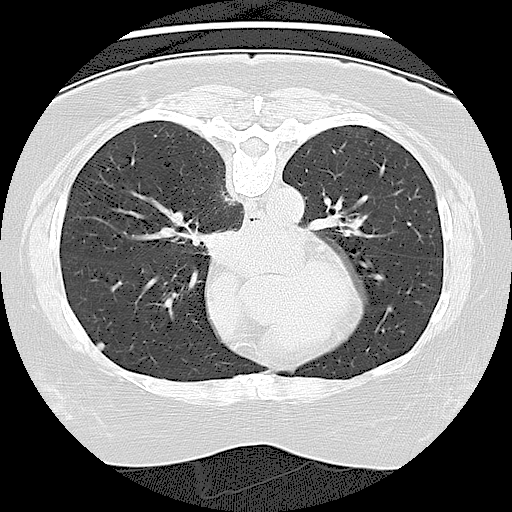
Axial slice from a low-dose chest CT screening exam, baseline screening round, lung window (W 1500 / L -600 HU), 120 kVp, slice 63 of 108 in the series. Female, age 67 years at enrolment. Former smoker at enrolment.
Expert-annotated lung lesion, bounding box [x1, y1, x2, y2] px = [80, 327, 123, 367]. The exam's reader record, not a measurement of the box and not confirmed to be the same lesion: non-calcified nodule or mass ≥4 mm, right middle lobe, 5 × 5 mm, smooth margins, soft tissue attenuation. Participant outcome: lung cancer diagnosed 575 days after this screen — small cell carcinoma, NOS, right upper lobe, undifferentiated (G4), stage IV (AJCC 6th edition), 60 mm at pathology.